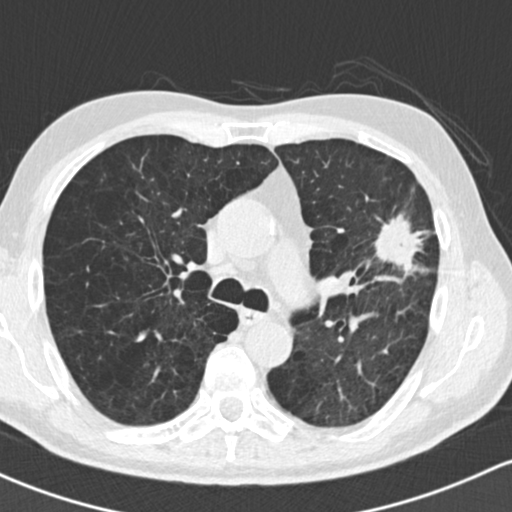
Low-dose screening chest CT, one axial slice; position 99 of 162 along the scan axis; 120 kVp; lung window (W 1500 / L -600 HU); 2 mm slice thickness; 512 × 512 image matrix, field of view 318 × 318 mm.
Structures marked on this image (expert manual segmentation):
- lesion 1 (tumor, upper lobe of left lung): bounding box <374,213,424,273> (left, top, right, bottom; pixels)